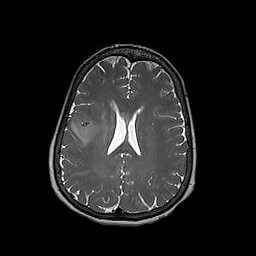
Brain MRI from a brain-tumour surgery series, one axial slice. Slice 81 of 192 in the series (ordered by position). 1 mm slice thickness. 256 × 256 image matrix, field of view 250 × 250 mm. From the clinical record (not read from this slice): histopathology: Oligodendroglioma; WHO grade: 3; IDH mutation: yes; tumour location: Right Frontal.
Annotated regions visible in this slice (manually delineated by an expert):
- tumour: bounding box [x1, y1, x2, y2] px = [72, 116, 97, 141]